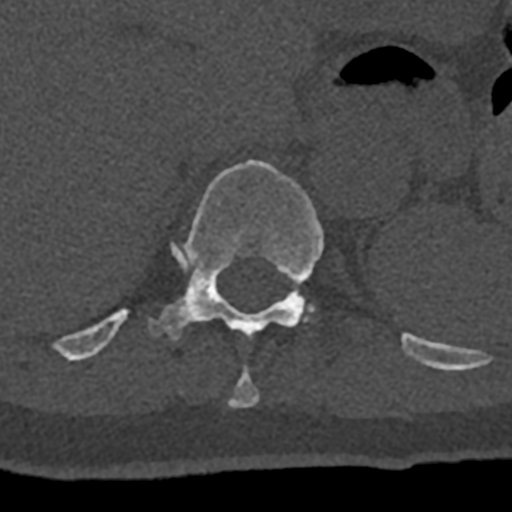
CT including the spine, one axial slice; slice 549 of 797 in the series (ordered by position); bone window (W 1800 / L 400 HU); 0.5 mm slice thickness; 512 × 512 image matrix, field of view 160 × 160 mm. Male patient, age 74 years. From the clinical record (not read from this slice): primary cancer: renal.
Structures marked on this image (semi-automatically segmented with operator editing):
- T10 vertebra: box from (x=229, y=367) to (x=259, y=408) px
- T11 vertebra: (x=70, y=160)–(x=432, y=367)
- T12 vertebra: (x=307, y=306)–(x=312, y=312)